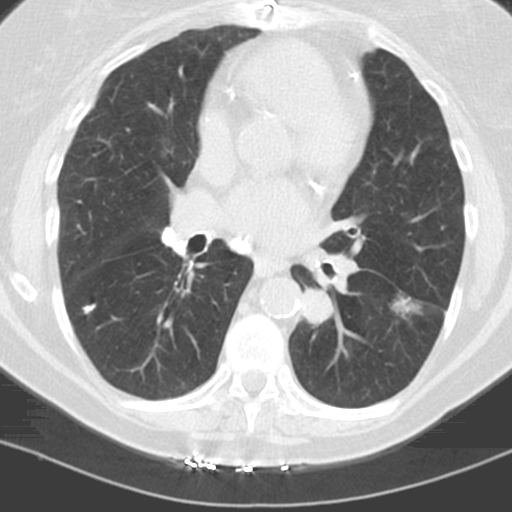
Low-dose screening chest CT, one axial slice; slice 56 of 121 in the series (ordered by position); 120 kVp; lung window (W 1500 / L -600 HU); 512 × 512 image matrix, field of view 278 × 278 mm.
Annotated regions visible in this slice (manually delineated by an expert):
- lesion 1 (tumor, lower lobe of left lung): bounding box [x1, y1, x2, y2] px = [394, 298, 419, 314]
- lesion 2 (tumor, lower lobe of left lung): [303, 288, 333, 325]